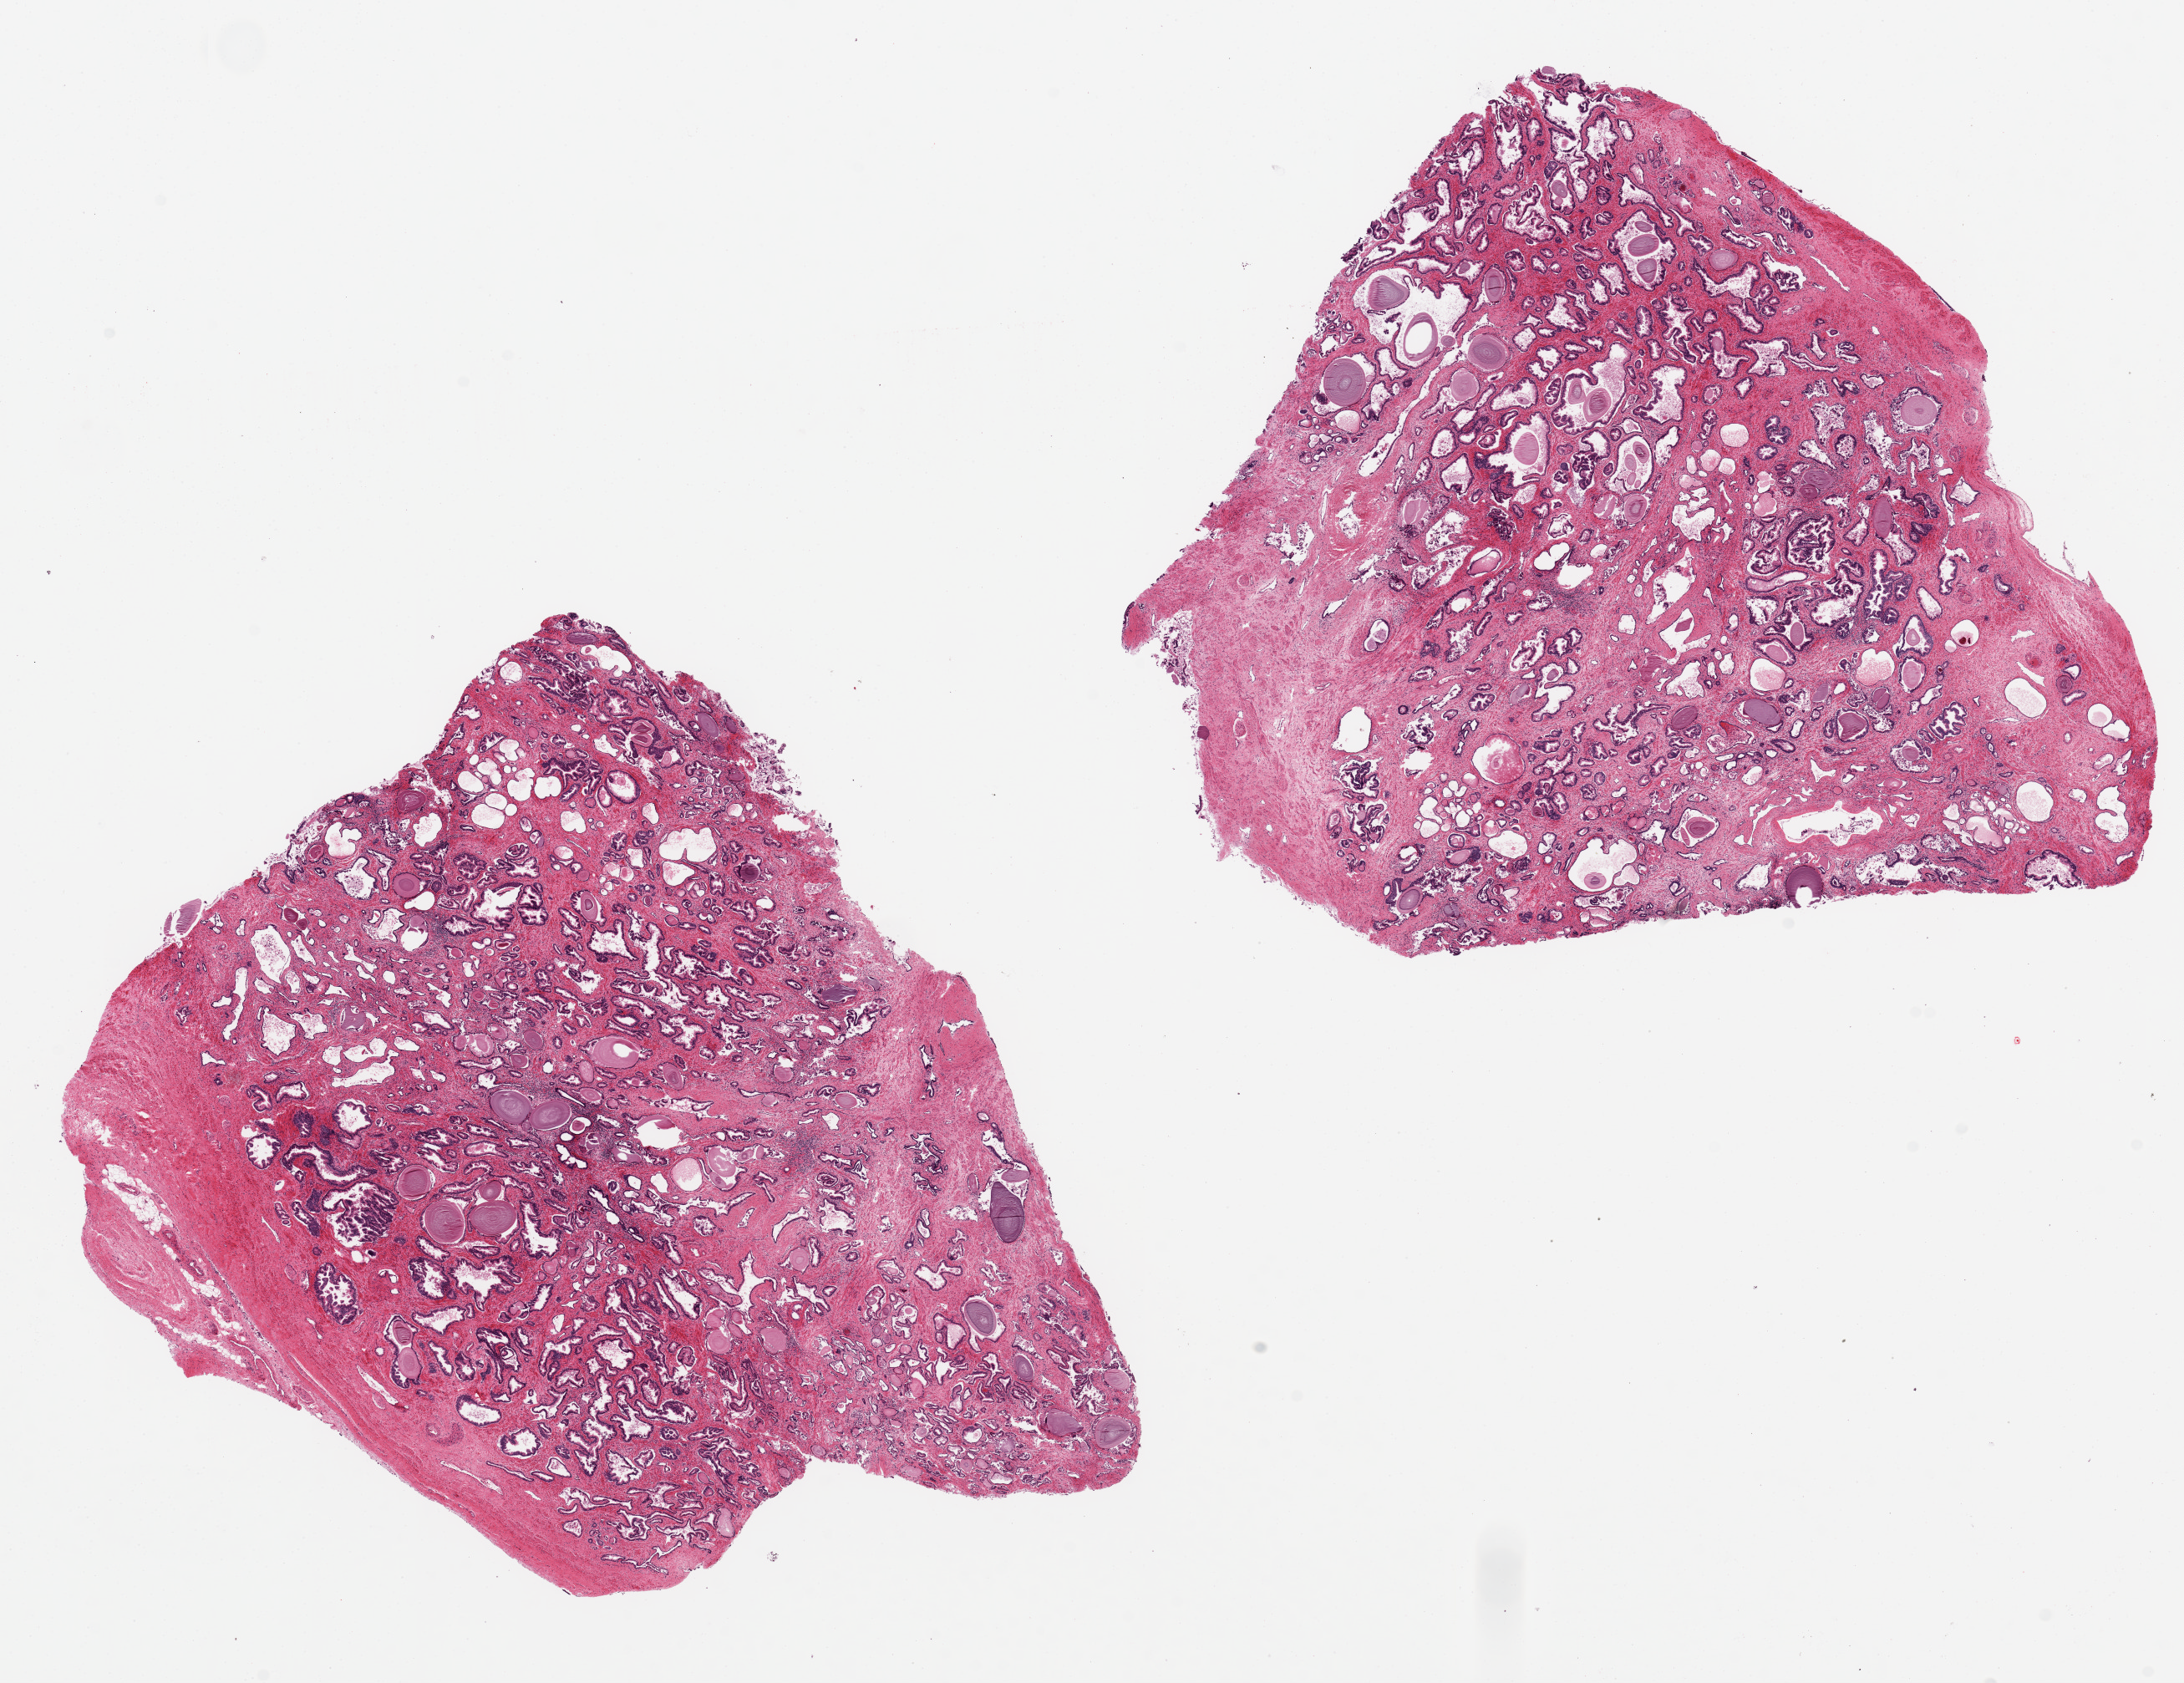
Whole-slide image, haematoxylin and eosin stain, whole scanned area (about 20.7 x 15.9 mm) shown as a low-resolution overview. PAXgene-fixed paraffin-embedded (PFPE) section. Target tissue: prostate. Donor tissue sample. Donor: male.
Reviewer comment on this tissue sample: 2 pieces, 9x7 & 9x8 mm; glandular hyperplasia.